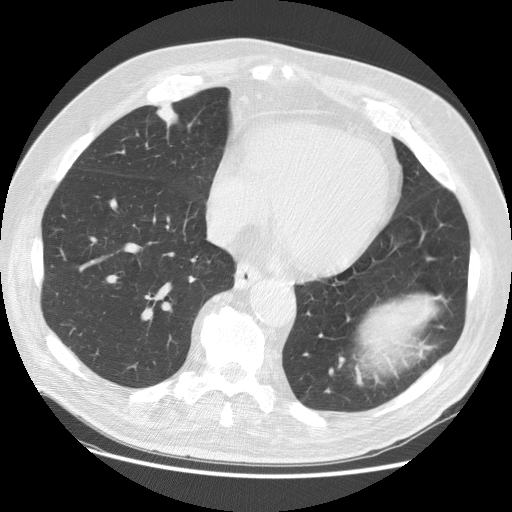
Low-dose screening chest CT, one axial slice. Reconstruction kernel STANDARD. Lung window (W 1500 / L -600 HU). 2.5 mm slice thickness. 512 × 512 image matrix, field of view 397 × 397 mm.
Structures marked on this image (expert manual segmentation):
- lesion 1 (tumor, upper lobe of right lung): bounding box [x1, y1, x2, y2] px = [156, 103, 177, 123]